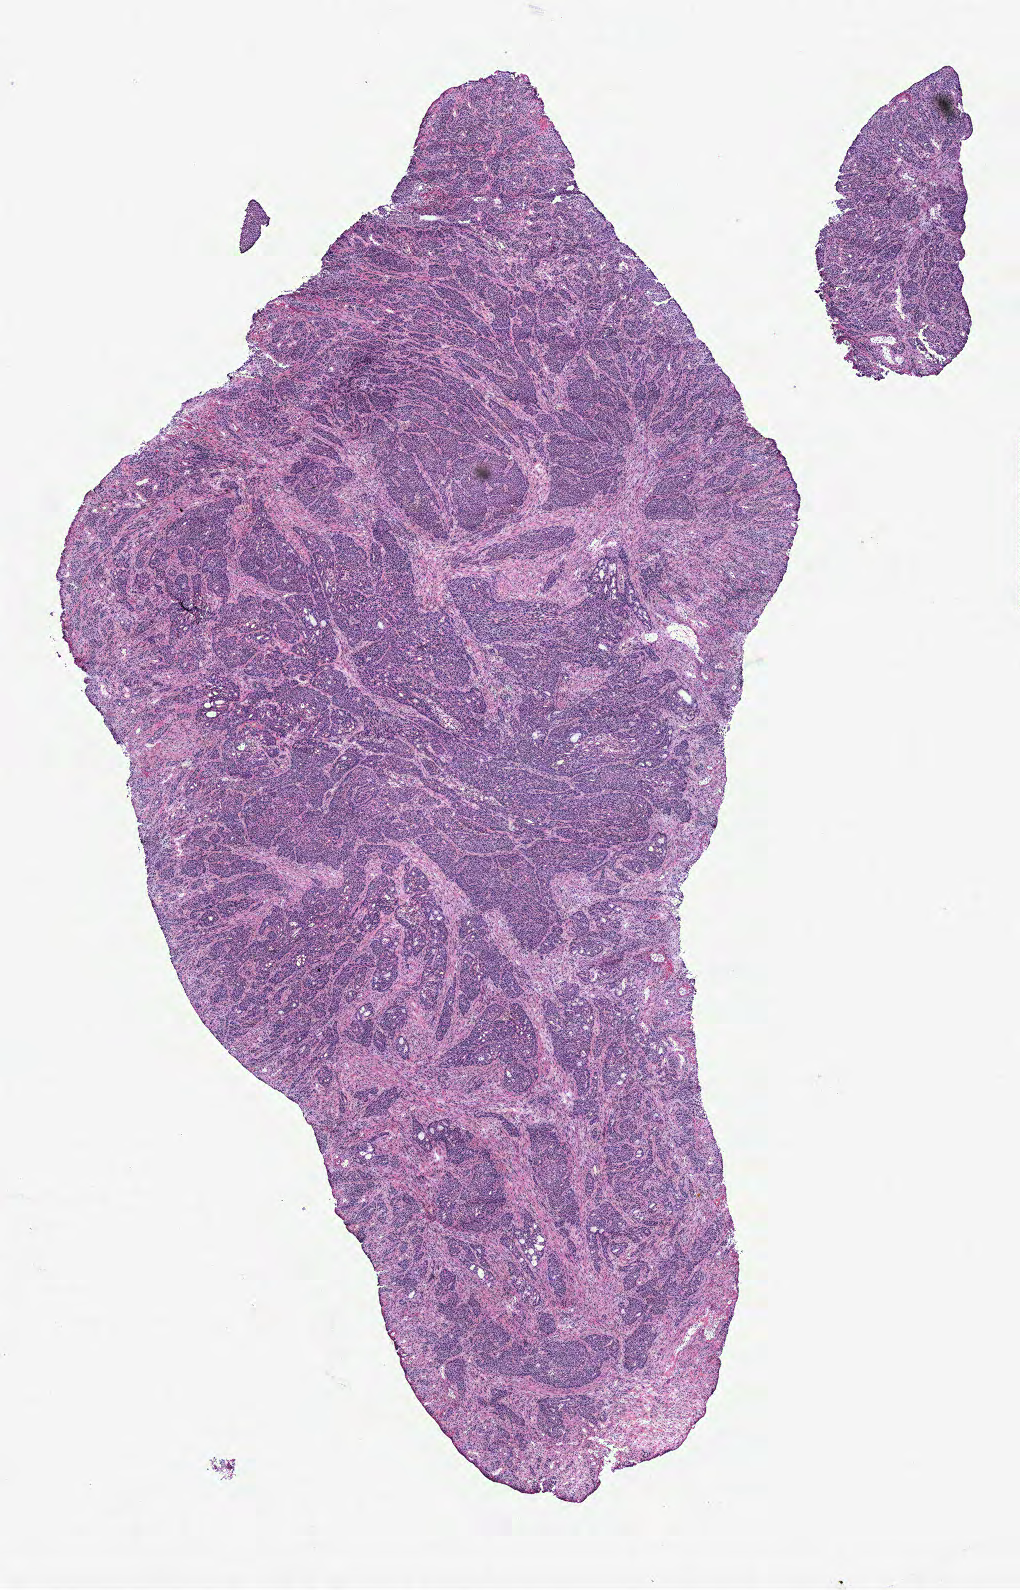
Whole-slide histology image, H&E — whole scanned area (about 8.2 x 12.7 mm) shown as a low-resolution overview. Colon, tumour tissue. Patient: female, age 78 years.
Primary tumour site (as recorded): colon. Histologic diagnosis: Adenocarcinoma, NOS. AJCC pathologic stage: IIA.